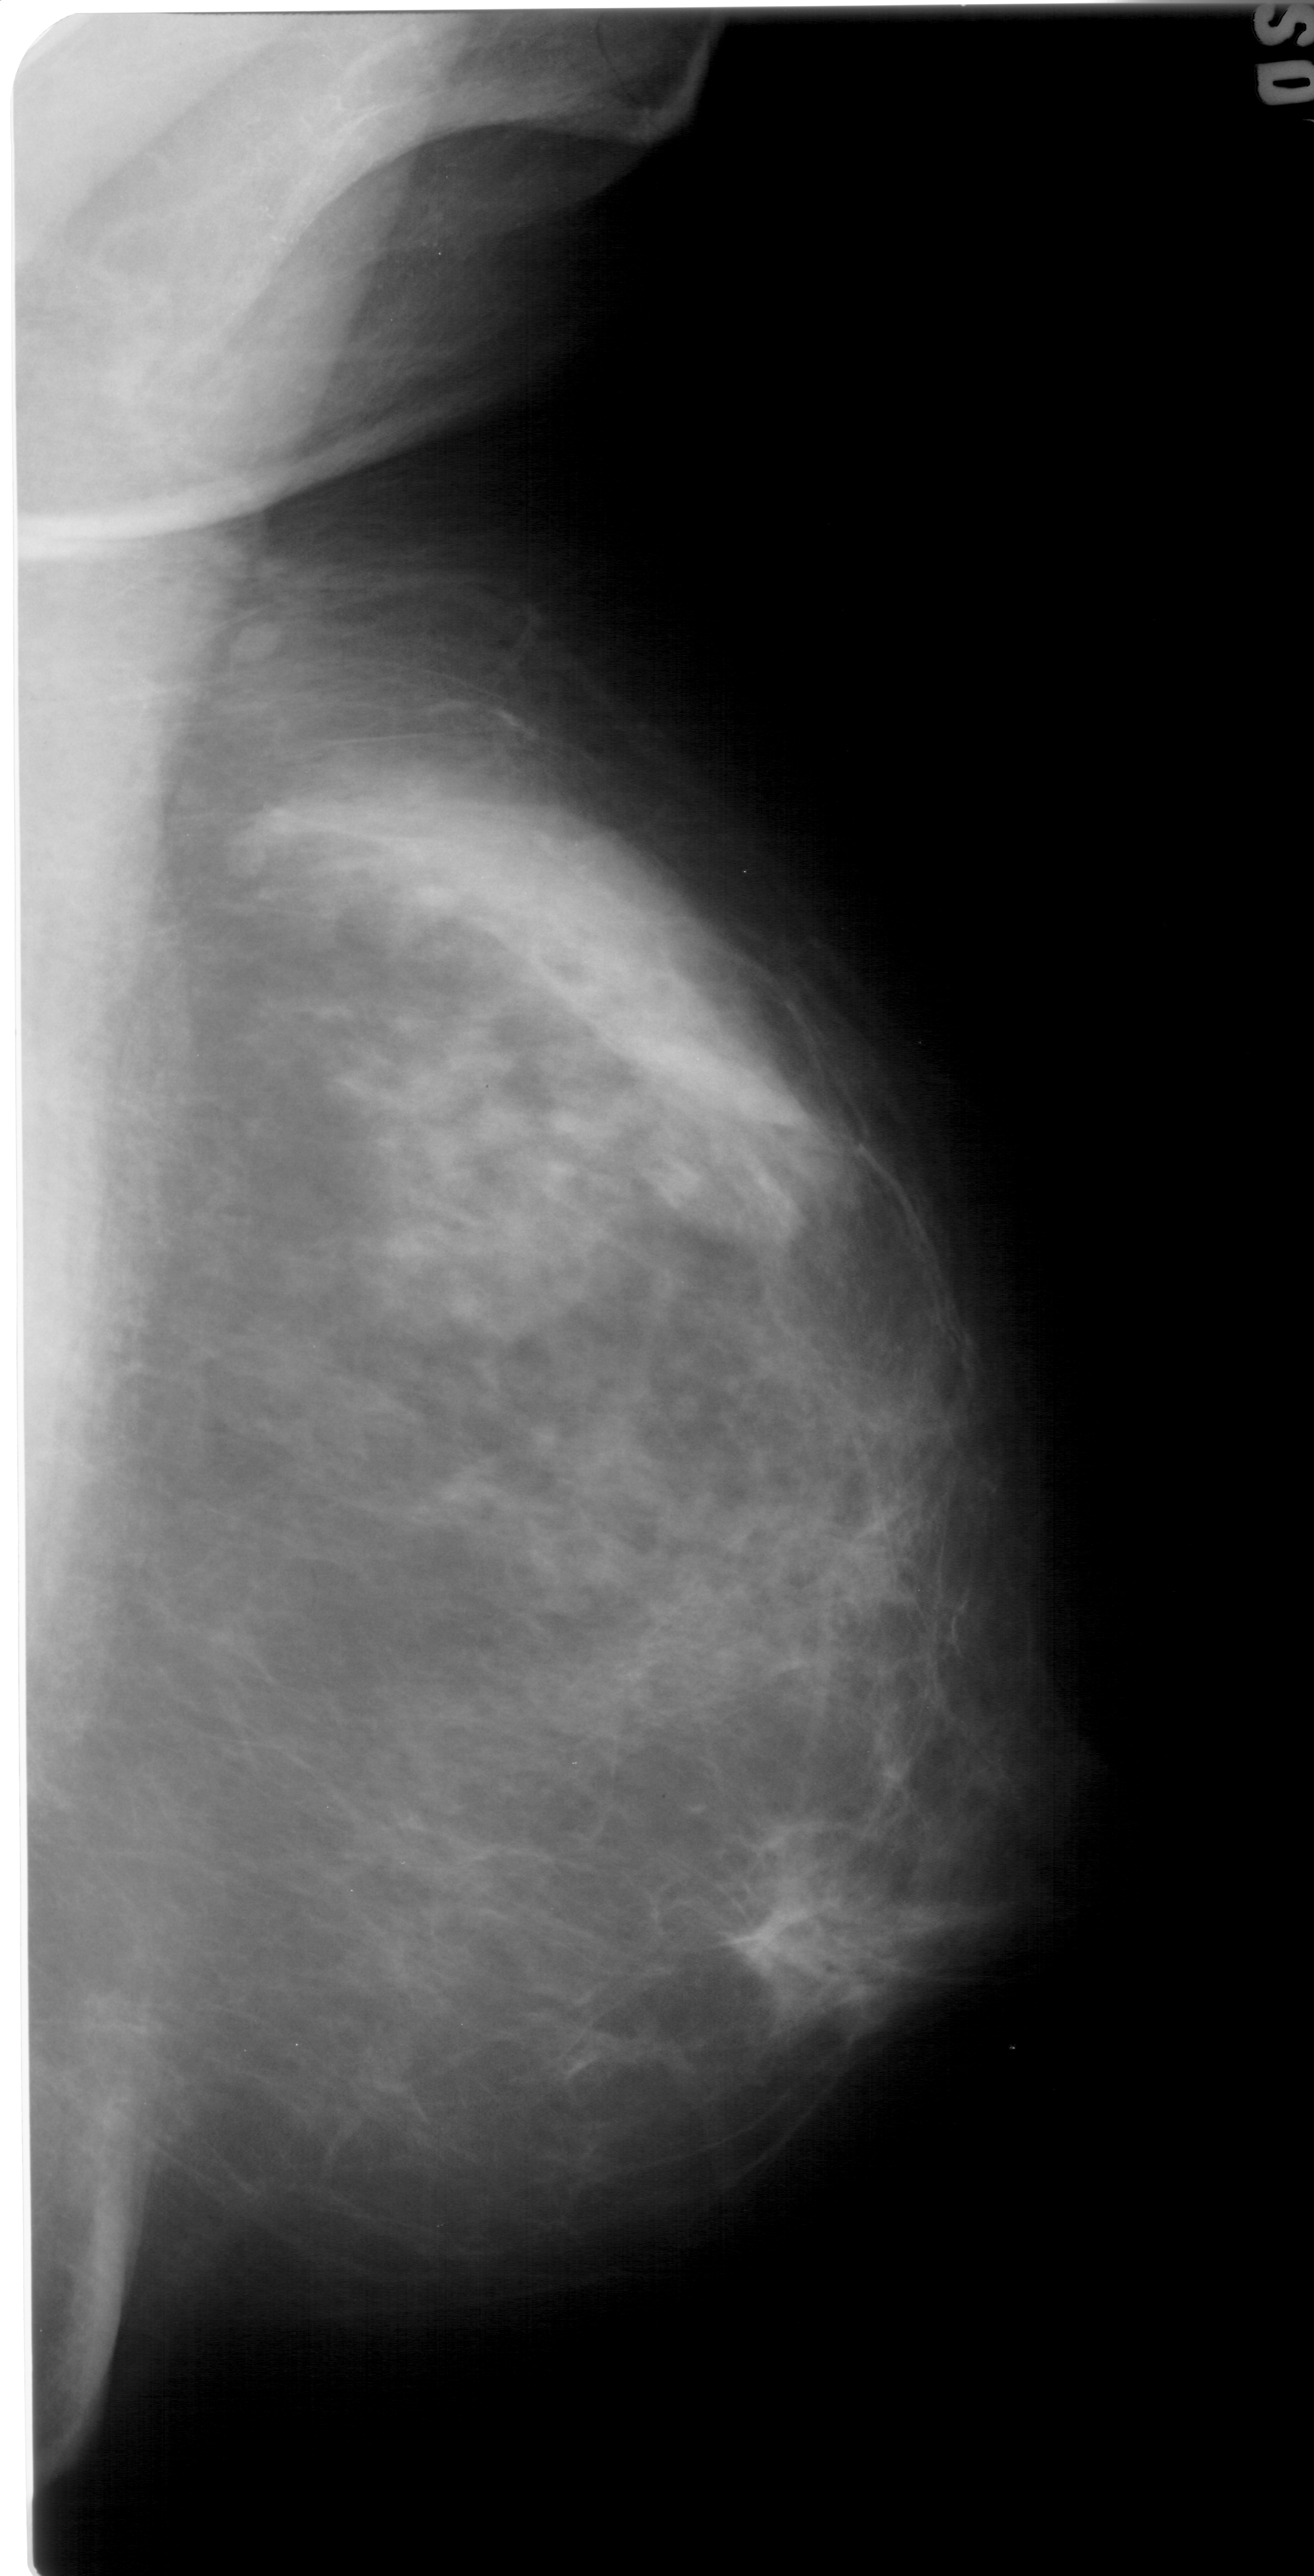
Scanned film-screen mammogram, right breast, mediolateral oblique (MLO) view, breast composition: scattered fibroglandular densities (BI-RADS density category 2 of 4).
Marked abnormality: mass, shape asymmetric breast tissue, margins obscured; BI-RADS assessment category 4; benign without callback (not worked up further).